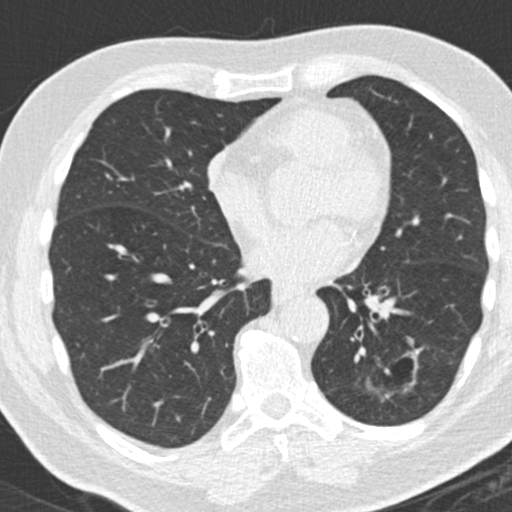
Chest CT (low-dose screening protocol), one axial image. Third annual screen. Lung window (W 1500 / L -600 HU). 2 mm slice thickness. 512 × 512 image matrix, field of view 300 × 300 mm. Male participant, aged 66 years at enrolment. Former smoker at enrolment.
• Expert-annotated lung lesion, bounding box [x1, y1, x2, y2] px = [355, 344, 427, 429].
• The exam's reader record, not a measurement of the box and not confirmed to be the same lesion: non-calcified nodule or mass ≥4 mm, left lower lobe, 31 × 24 mm, spiculated (stellate) margins, pre-existing on the prior screen: yes; interval growth: yes.
• Later outcome: lung cancer diagnosed 56 days after this screen — adenocarcinoma, NOS, left lower lobe, poorly differentiated (G3), stage IB (AJCC 6th edition), 38 mm at pathology.